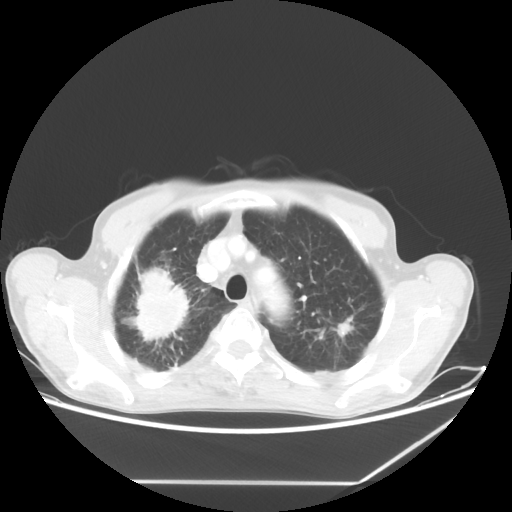
Chest CT, one axial slice; position 51 of 65 along the scan axis; 80 kVp; lung window (W 1500 / L -600 HU); 5 mm slice thickness; 512 × 512 image matrix, field of view 397 × 397 mm. Male patient, age 68 years. Case-level facts recorded for this patient, not image findings: clinical TNM (as recorded): T3 N3 M0.
Structures marked on this image (bounding box drawn by a radiologist):
- lung tumour (recorded histology: adenocarcinoma): box from (x=134, y=268) to (x=190, y=345) px